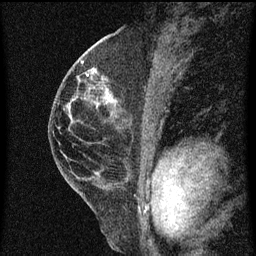
Breast MRI (dynamic contrast-enhanced), one sagittal slice. Position 33 of 60 along the scan axis. Dynamic contrast-enhanced series, image 2 of 3 at this slice position (ordered by acquisition). 1.5 T. TE 4.2 ms, TR 8 ms. 2 mm slice thickness. 256 × 256 image matrix. Patient: female, 48 years.
Structures marked on this image (semi-automatically segmented with operator editing):
- analysis volume of interest (the breast-tissue region the enhancement analysis was run in; not a lesion): bounding box [x1, y1, x2, y2] px = [89, 72, 123, 113]
- tumour enhancement mask (voxels above the 70 % enhancement threshold inside the analysis volume of interest): [89, 76, 114, 101]